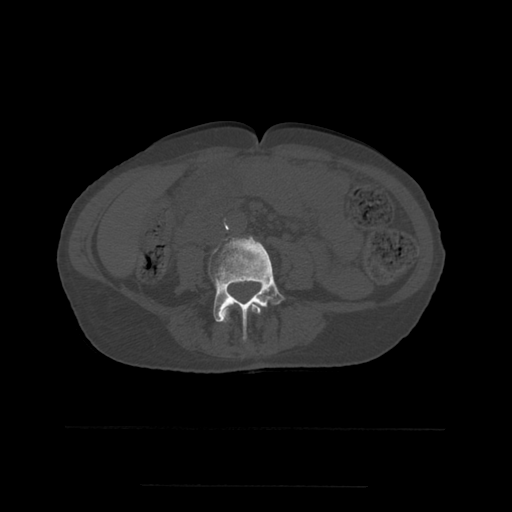
CT including the spine, one axial slice; position 171 of 544 along the scan axis; bone window (W 1800 / L 400 HU); 512 × 512 image matrix, field of view 350 × 350 mm. Patient age 58 years. Case-level facts recorded for this patient, not image findings: primary cancer: lung.
Annotated regions visible in this slice (semi-automatically segmented with operator editing):
- L3 vertebra: bounding box <221,303,261,323> (left, top, right, bottom; pixels)
- L4 vertebra: <209,236,285,340>